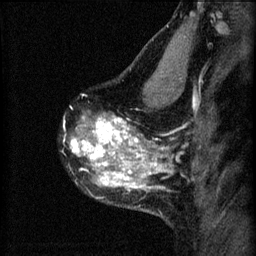
Breast MRI (dynamic contrast-enhanced), one sagittal slice; slice 43 of 60 in the series (ordered by position); 3 images stored at this slice position (order not interpretable as contrast timing); 1.5 T; TE 4.2 ms, TR 8.2 ms; 2 mm slice thickness; 256 × 256 image matrix, field of view 180 × 180 mm. Female patient, age 40 years.
Annotated regions visible in this slice (semi-automatically segmented with operator editing):
- analysis volume of interest (the breast-tissue region the enhancement analysis was run in; not a lesion): bounding box <66,76,179,219> (left, top, right, bottom; pixels)
- tumour enhancement mask (voxels above the 70 % enhancement threshold inside the analysis volume of interest): <70,116,163,193>